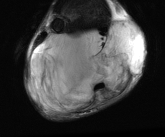
MRI of an extremity soft-tissue mass, one axial slice. Position 21 of 81 along the scan axis. T2-weighted fat-saturated. MR volume resampled by the dataset authors to the PET/CT grid (not the native acquisition matrix). 3.27 mm slice thickness. 165 × 137 image matrix. Male patient. From the clinical record (not read from this slice): histological type: liposarcoma - round cell; grade: high; site of the primary tumour: right calf.
Structures marked on this image (expert contour drawn on MRI and transferred to this co-registered scan by the dataset authors):
- gross tumour volume (mass): bounding box (x1, y1, x2, y2) in pixels: (28, 21, 145, 115)